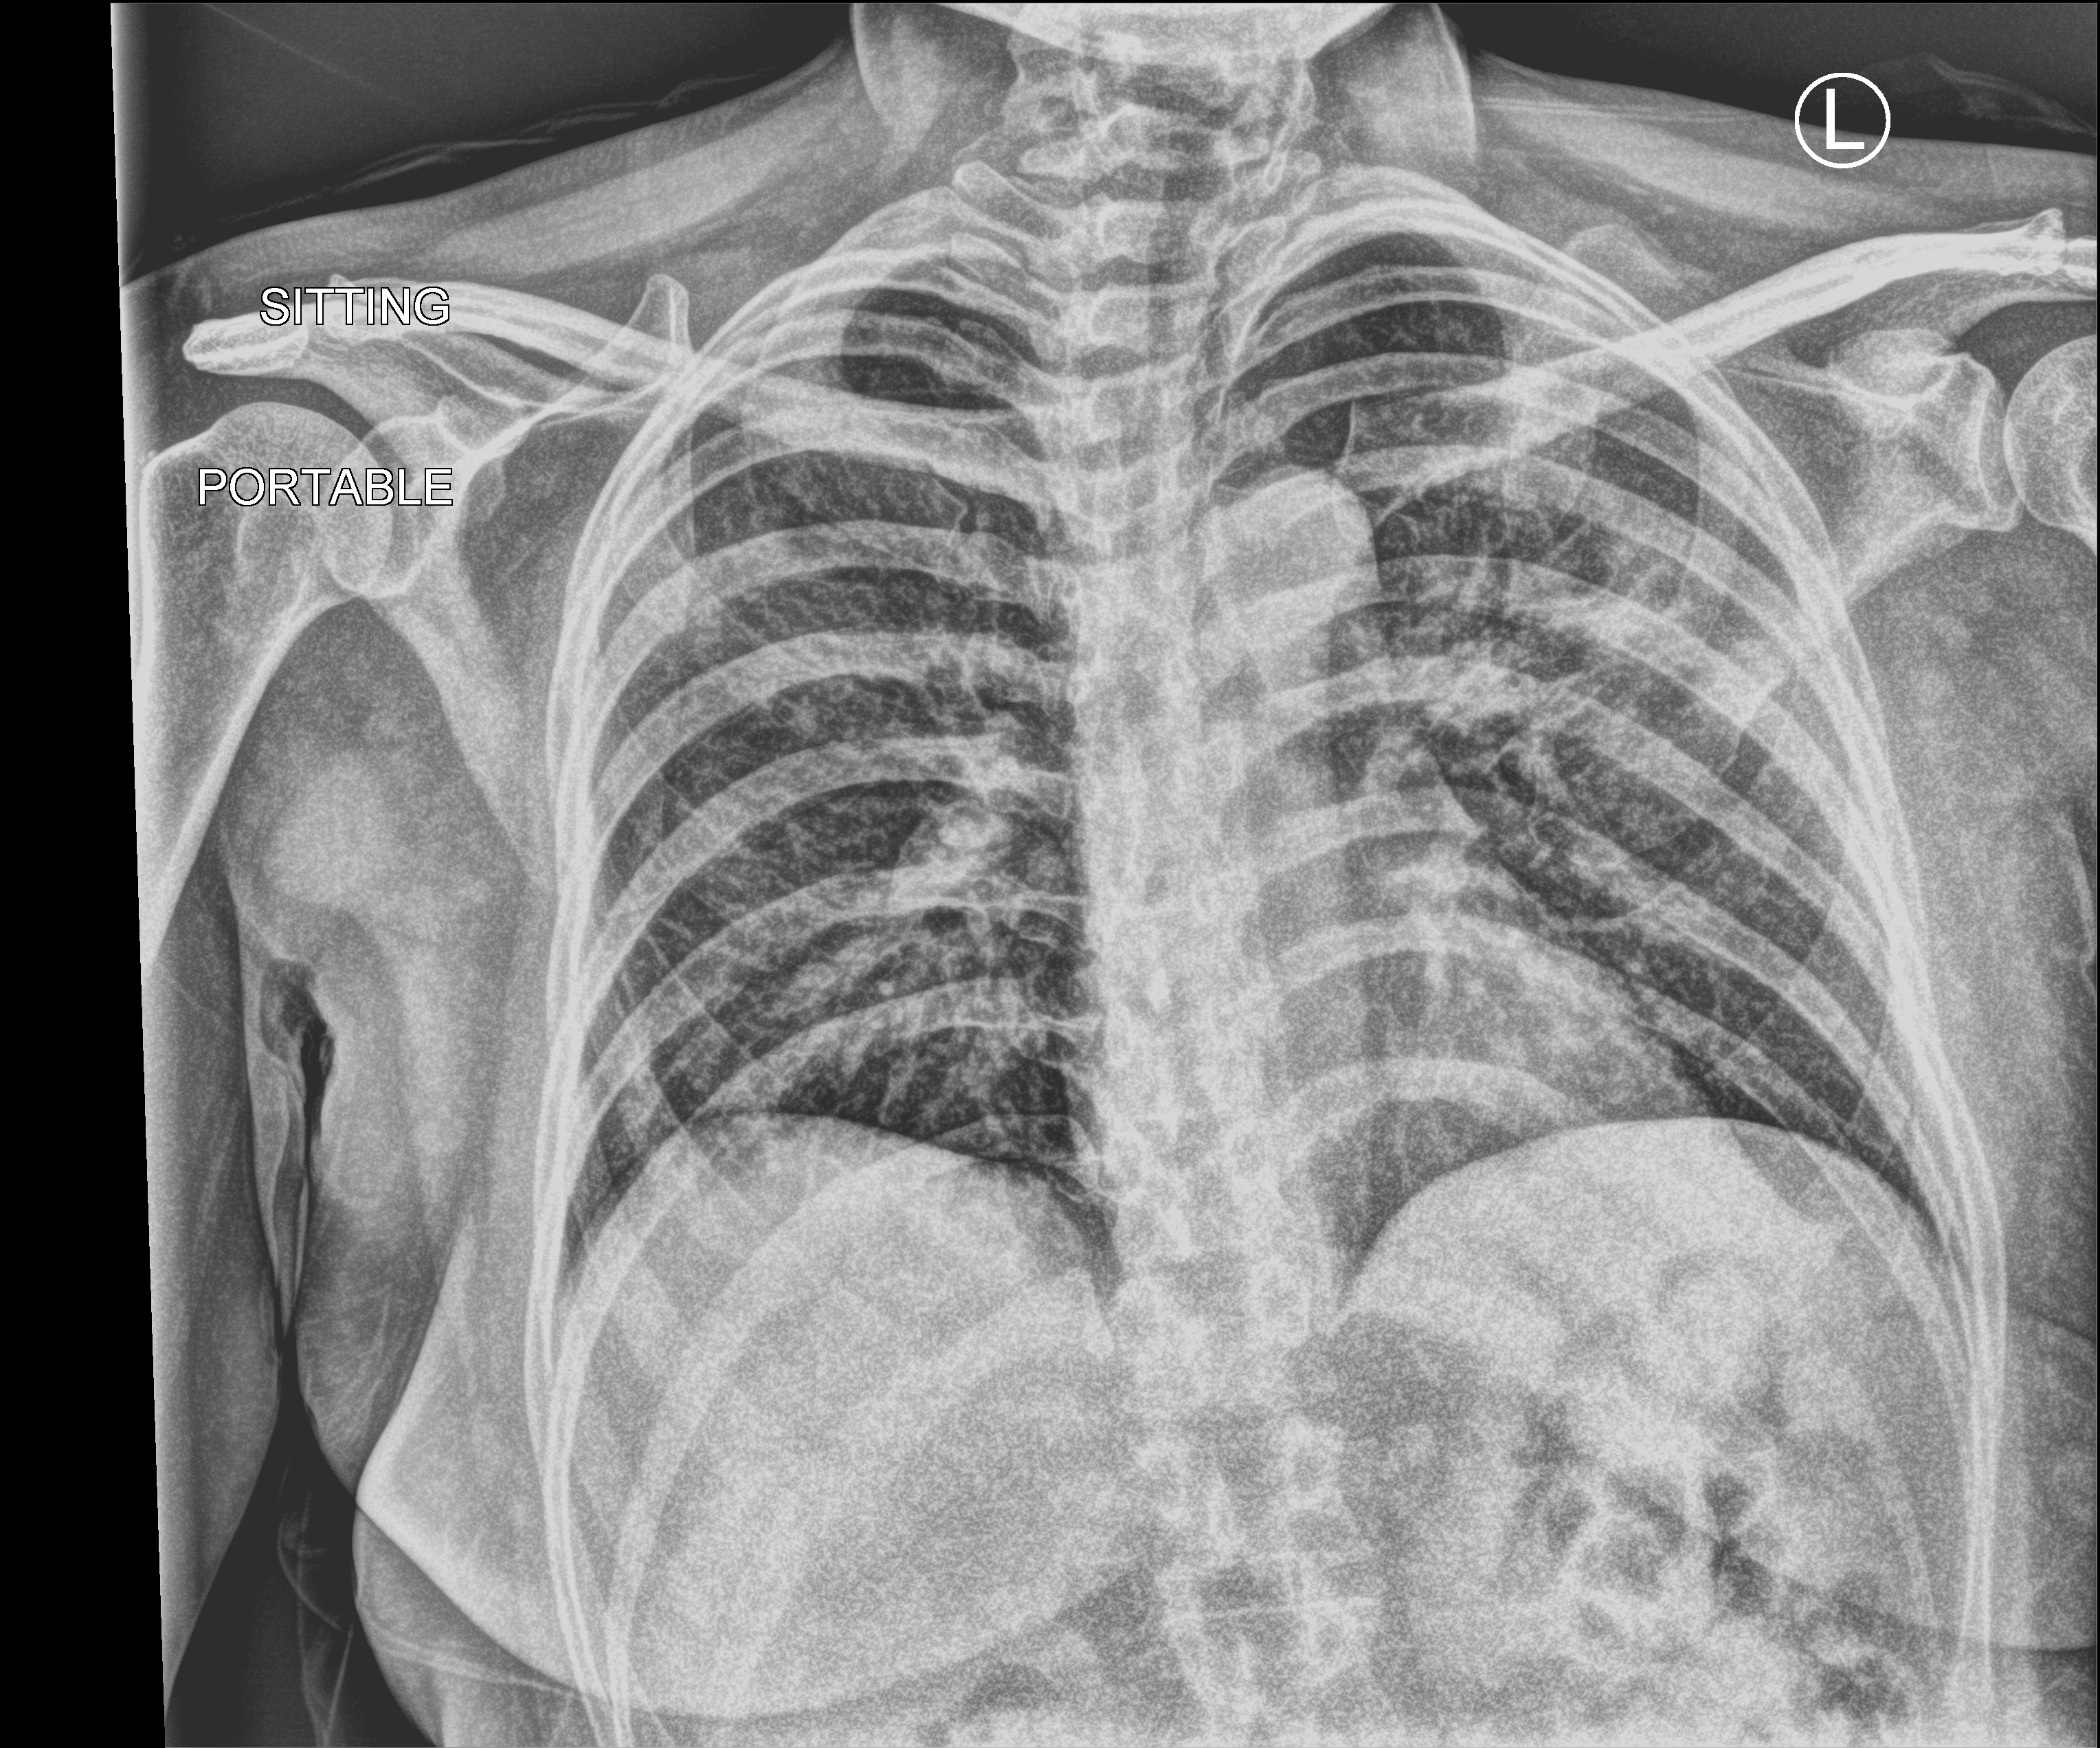
Chest X-ray (portable), anteroposterior (AP) projection. Female patient hospitalised with COVID-19, age 18–59 years.
Admission-level facts for this patient (not findings on this image; timing relative to this image not recorded): COPD (admission record): no.